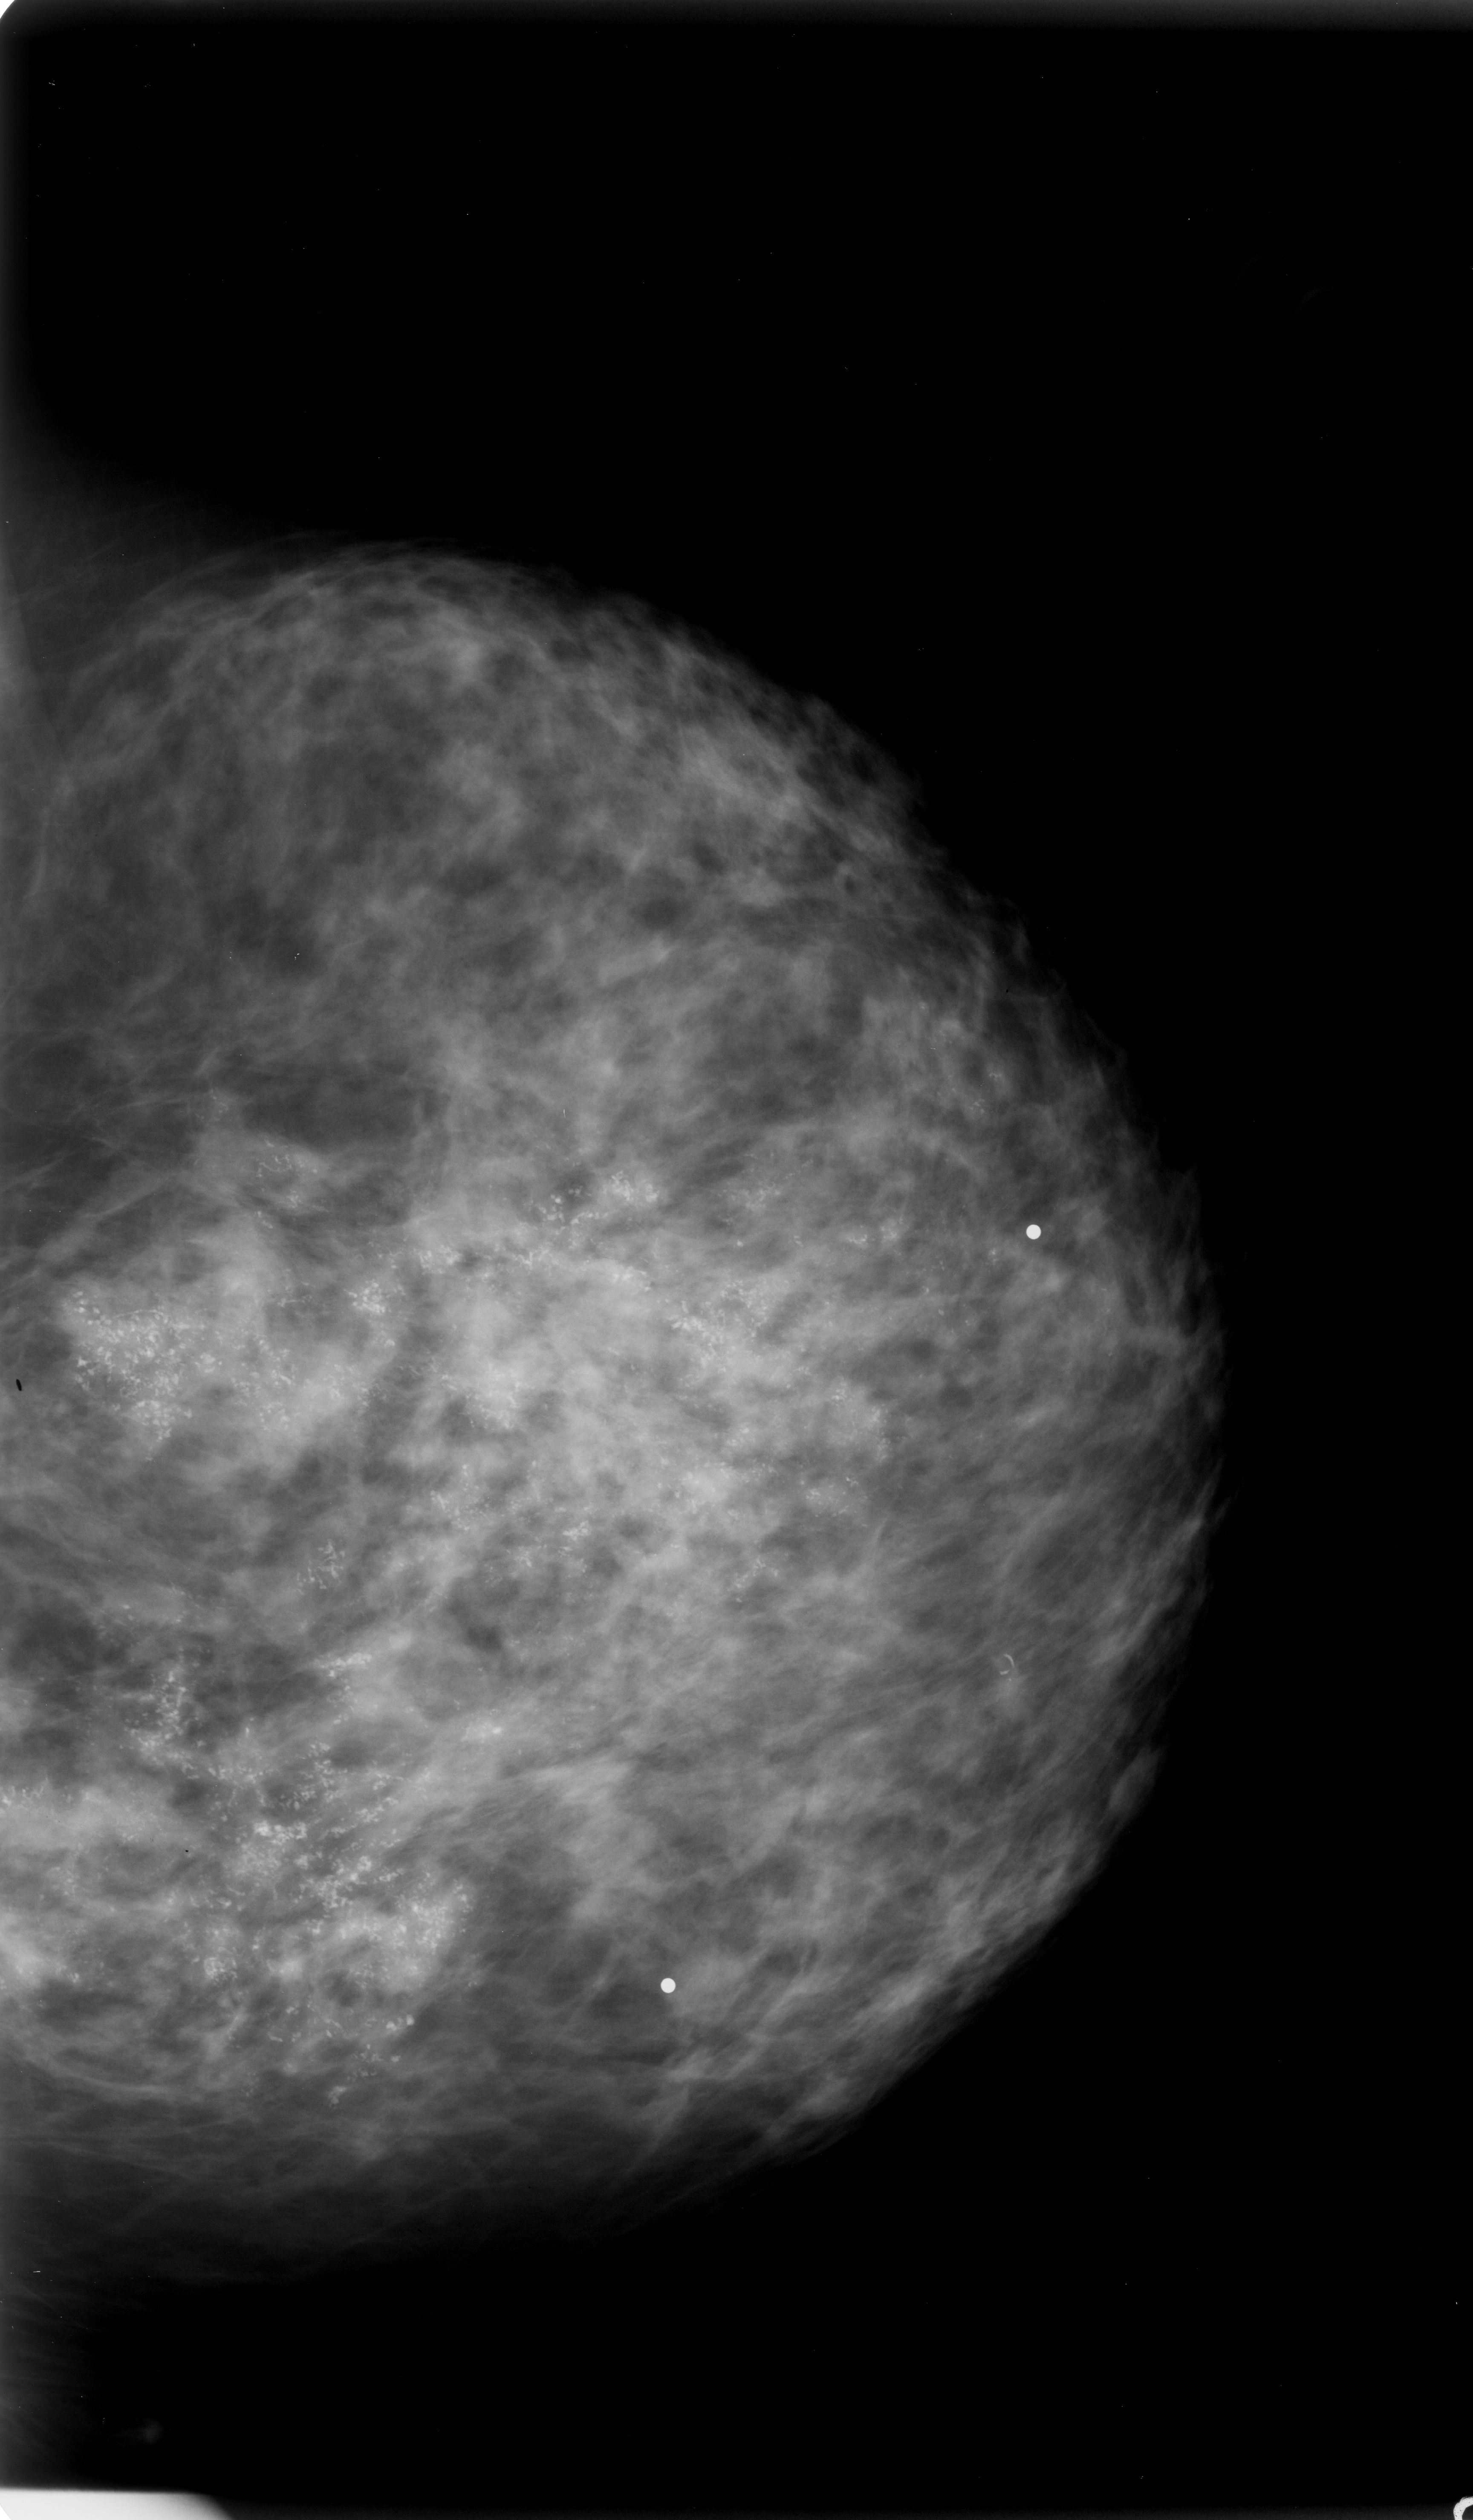
Digitized screen-film mammogram. Left breast. CC view. 1473 × 2520 image matrix.
Marked abnormalities (boxes around the expert regions of interest):
- calcifications, morphology pleomorphic, distribution regional; BI-RADS assessment category 5; subtlety rating 5 on a 1 (subtle) to 5 (obvious) scale; pathology (as recorded): malignant: bounding box (x1, y1, x2, y2) in pixels: (0, 876, 1225, 2272)